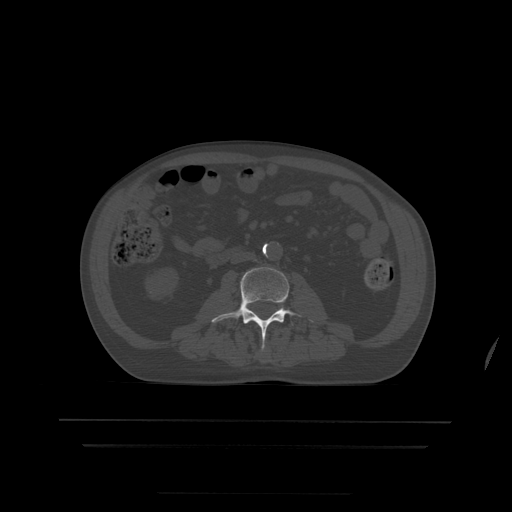
CT including the spine, one axial slice; position 120 of 522 along the scan axis; bone window (W 1800 / L 400 HU); 1.25 mm slice thickness; 512 × 512 image matrix, field of view 436 × 436 mm. Patient age 68 years. From the clinical record (not read from this slice): primary cancer: urothelial.
Structures marked on this image (semi-automatic segmentation, software-assisted and operator-edited):
- L3 vertebra: bounding box (x1, y1, x2, y2) in pixels: (211, 267, 313, 349)